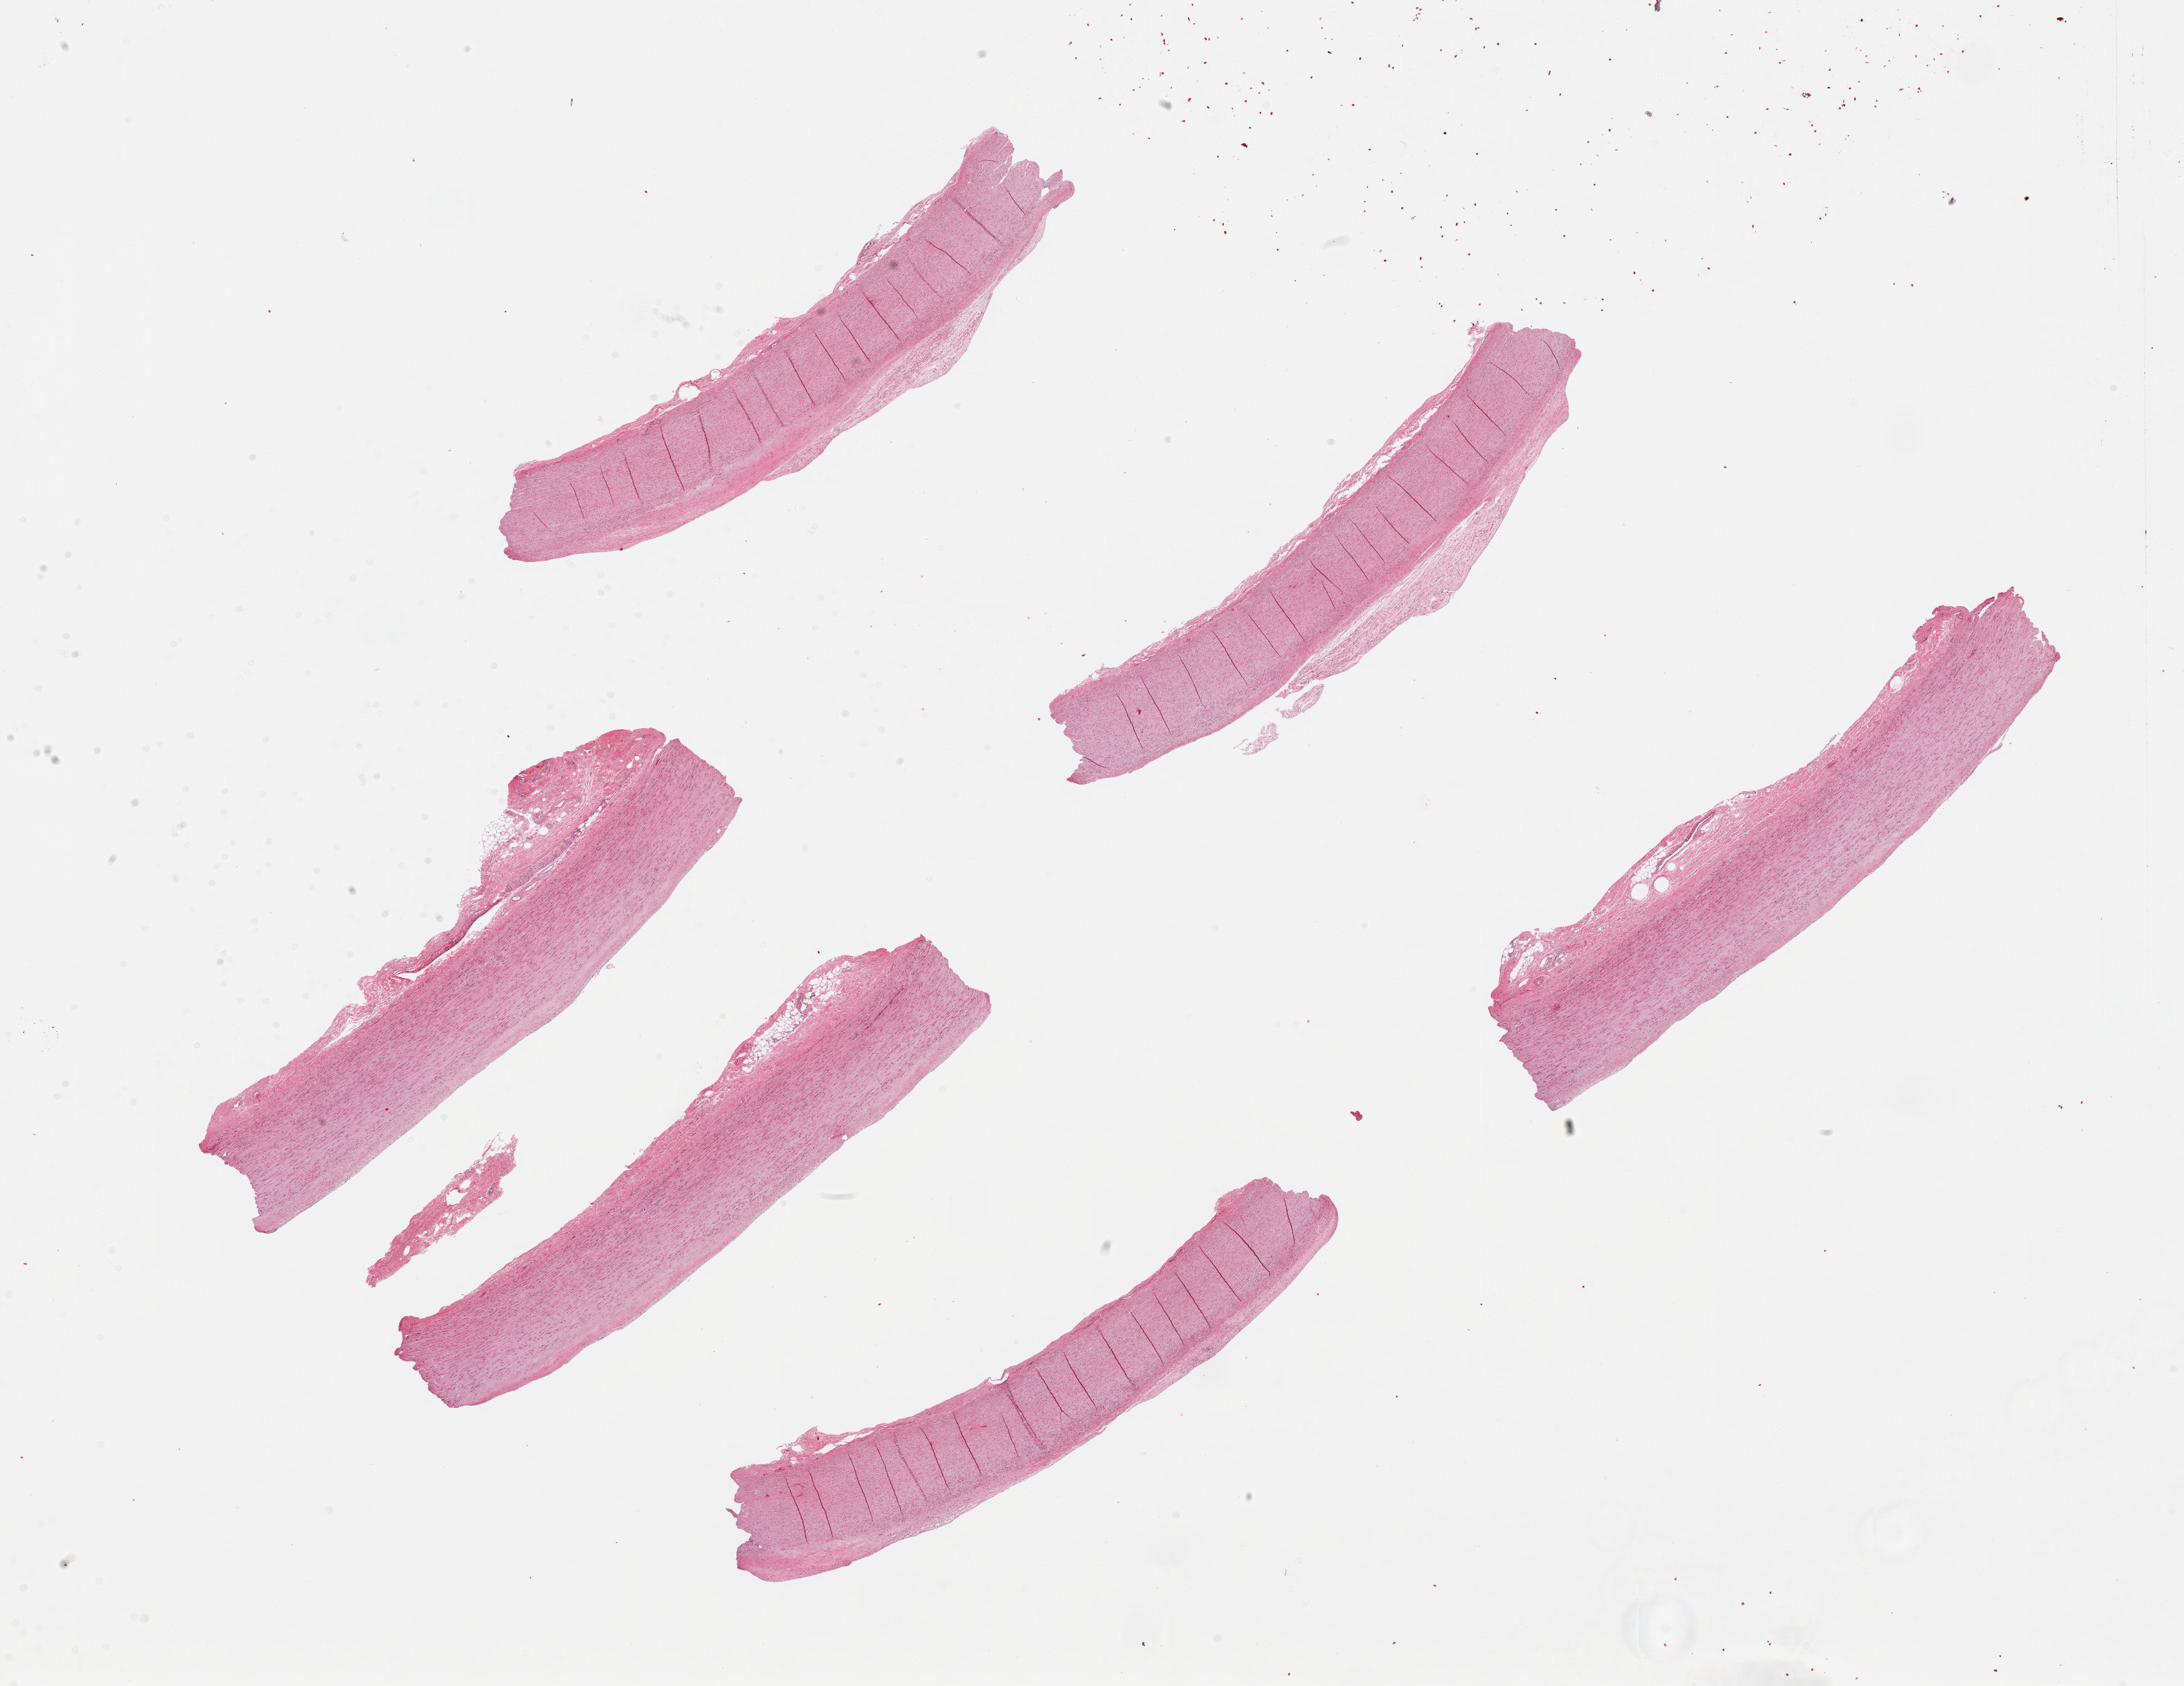
Digitized H&E-stained section — shown as a low-resolution overview of the whole scanned area (about 27.6 x 21.3 mm, slide scanned at 20x); PAXgene-fixed, paraffin-embedded tissue; section of aorta (target tissue); tissue donor sample.
- reviewer comment on this tissue sample: 6 pieces, atherosis up to ~0.3mm